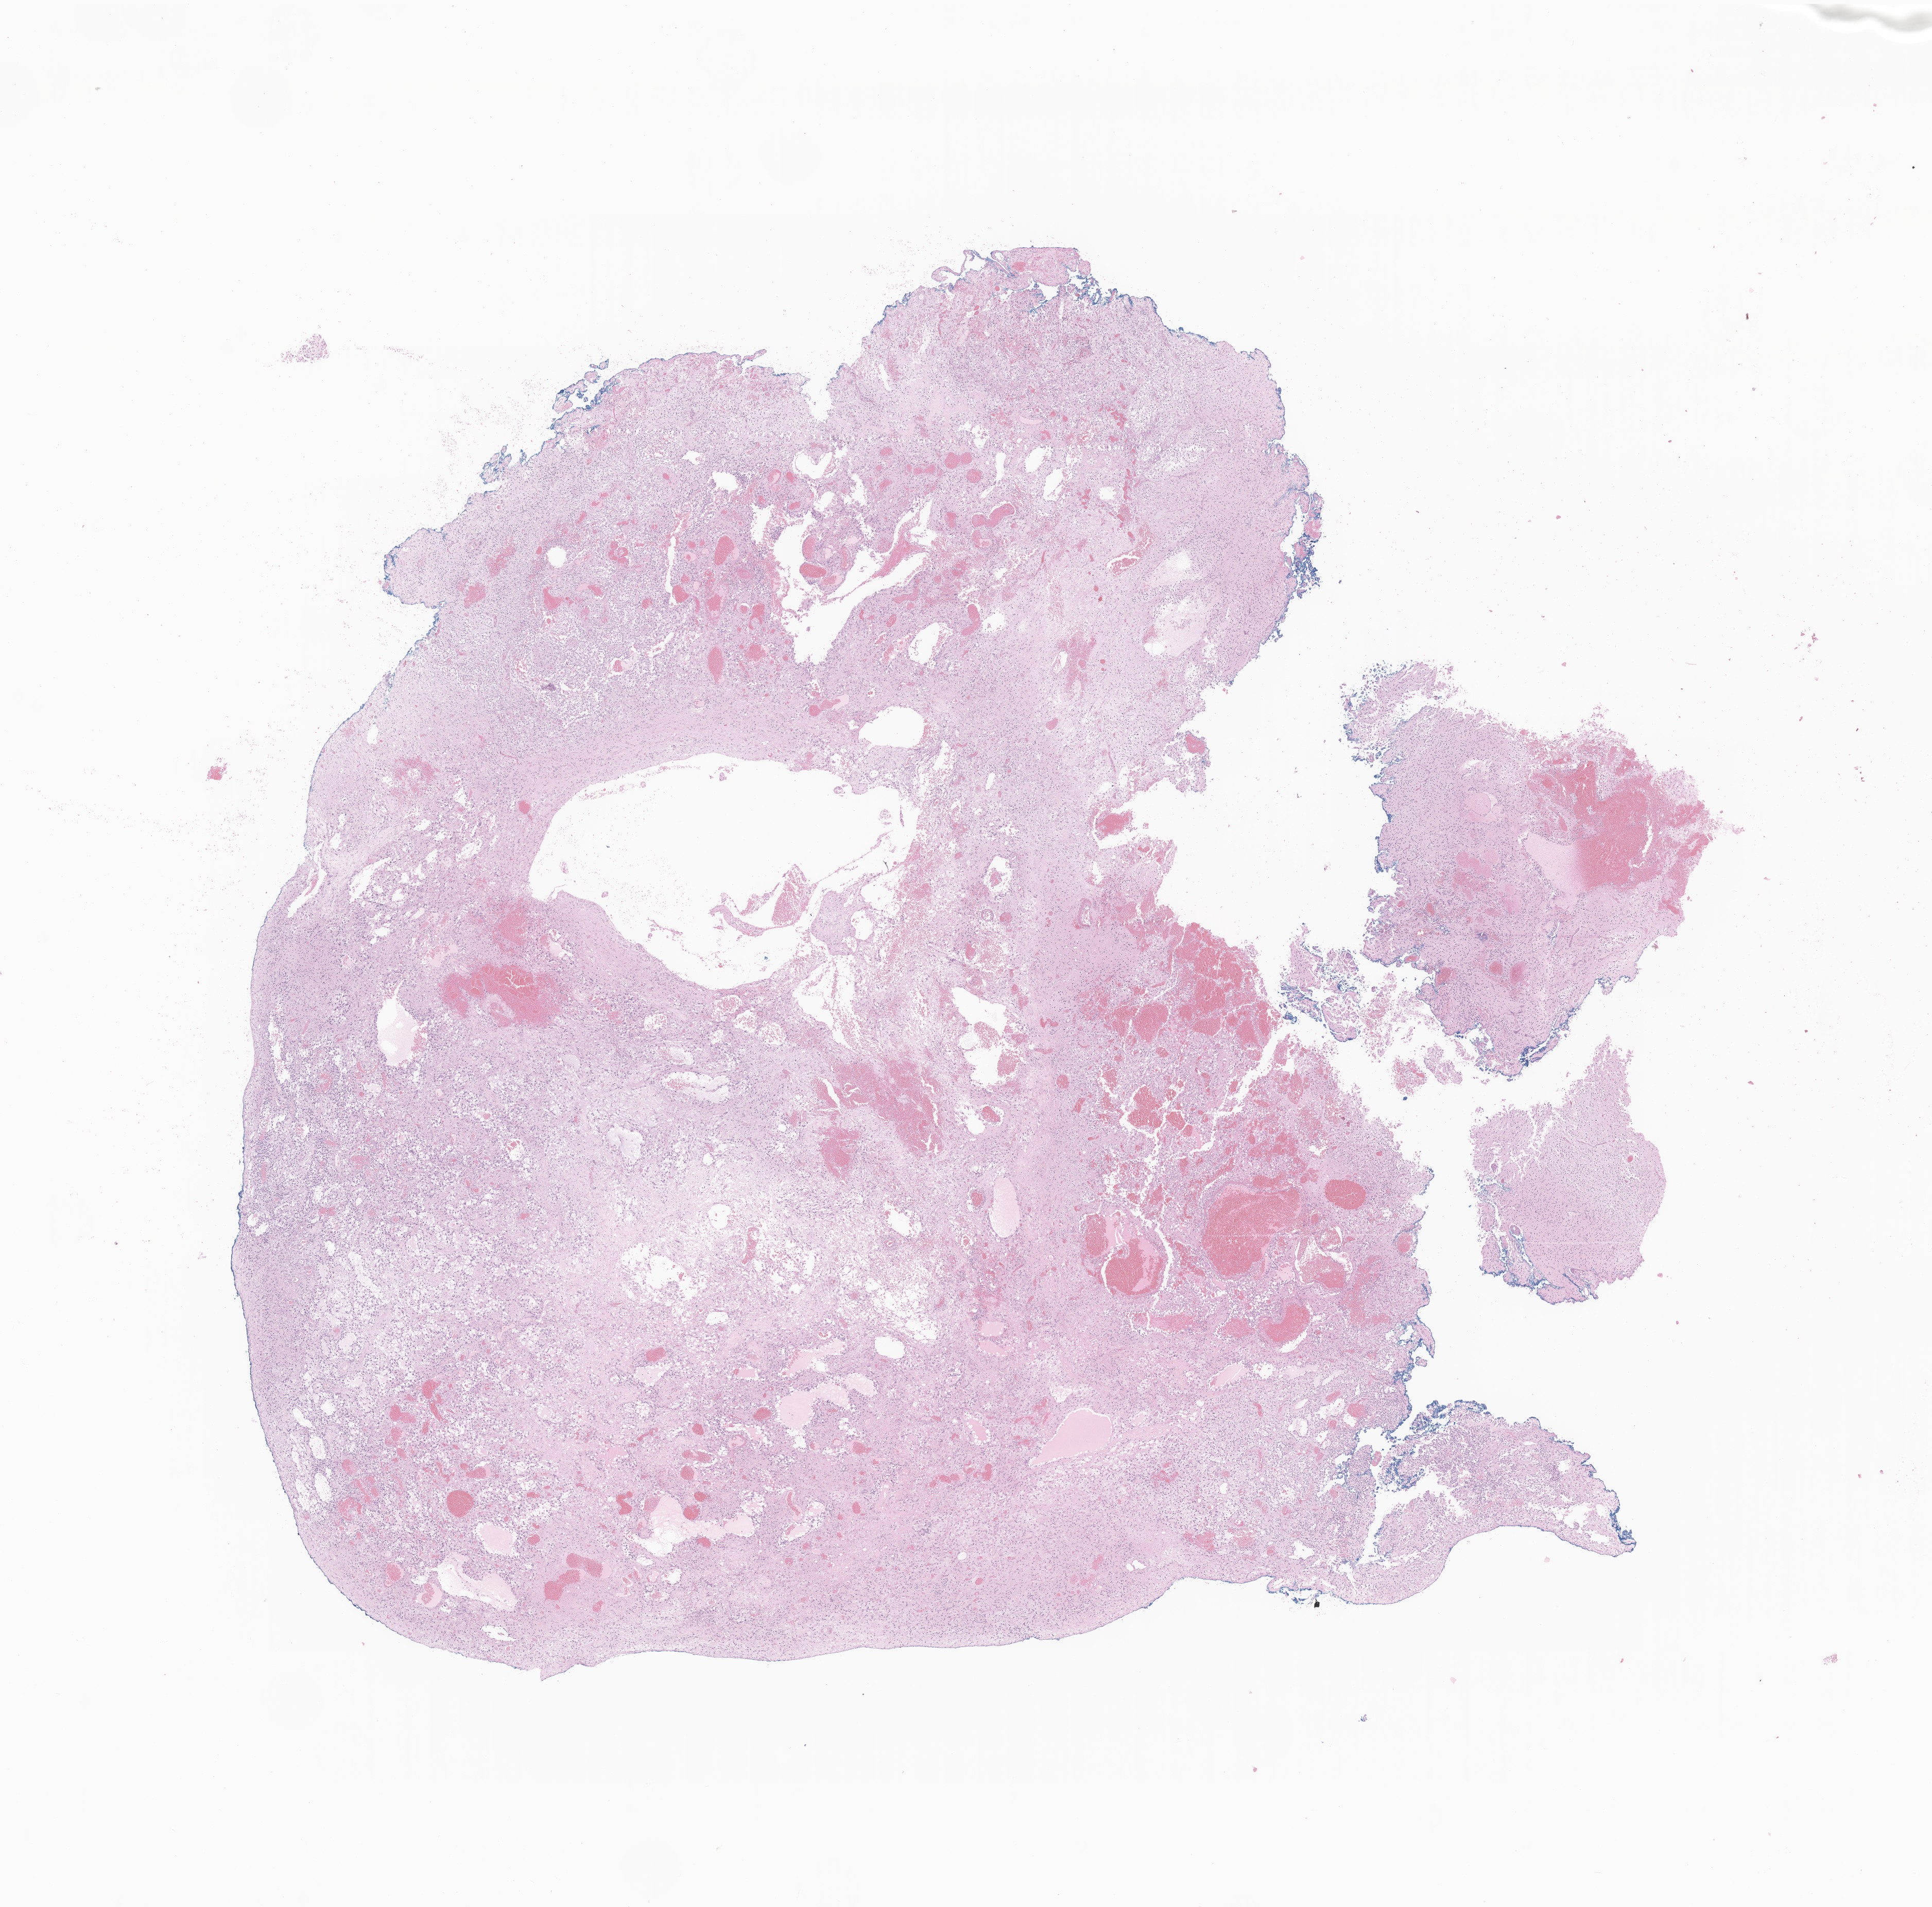
Whole-slide image, haematoxylin and eosin stain of tumor tissue from the parietal lobe, shown as a low-resolution overview of the whole scanned area (about 15.8 x 15.6 mm). Formalin-fixed paraffin-embedded section. Patient: male, age 125 months.
• diagnosis: Pilocytic astrocytoma